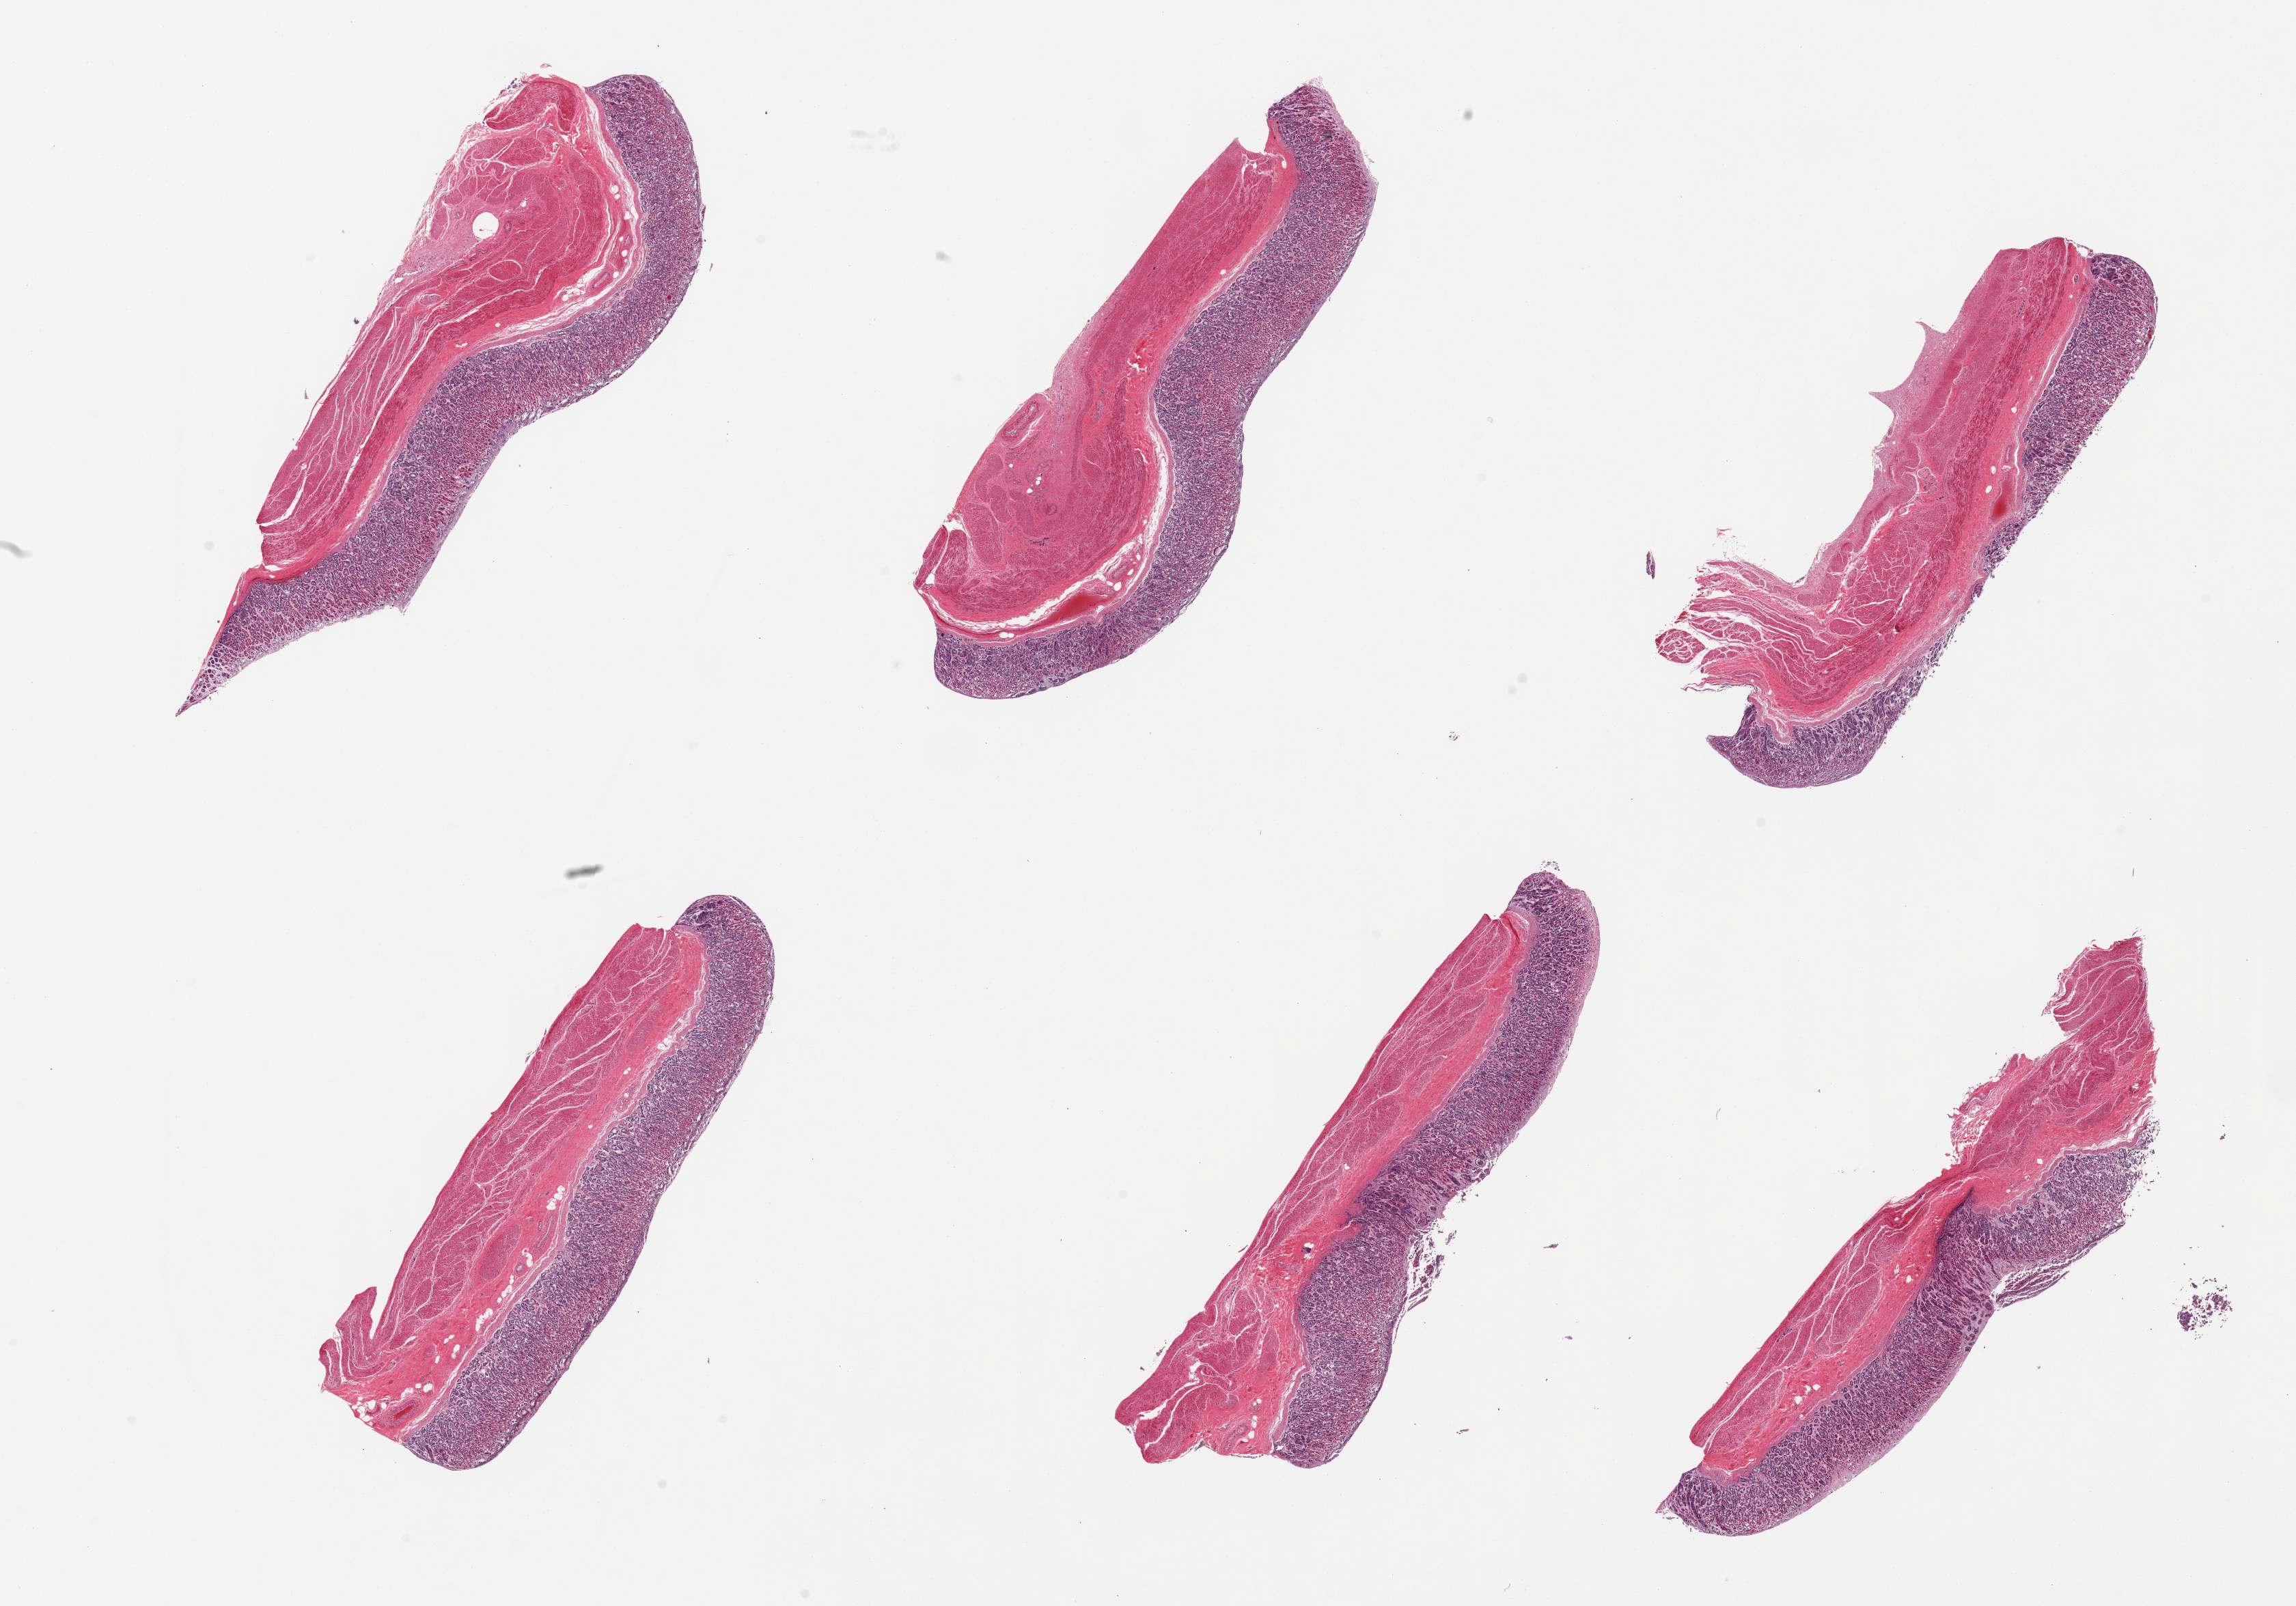
Digitized hematoxylin and eosin (H&E)-stained section, brightfield, whole scanned area (about 26.6 x 18.6 mm) shown as a low-resolution overview, PAXgene-fixed, paraffin-embedded tissue, sampled site (target tissue): stomach, tissue donor sample. Female donor.
Review note (as recorded): 6 pieces, mucosa up to ~1mm thick in areas; generally well preserved but approach a '2' in some foci.